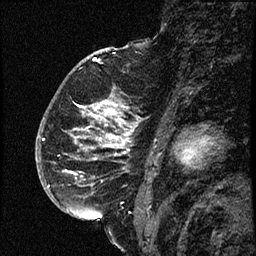
Breast MRI (dynamic contrast-enhanced), one sagittal slice; dynamic contrast-enhanced study with each time point stored as its own series, time point 2 of 3 at this slice position (early post-contrast, ordered by acquisition time); 1.5 T; TE 4.2 ms, TR 17.6 ms; 256 × 256 image matrix, field of view 200 × 200 mm. Female patient. Case-level facts recorded for this patient, not image findings: setting: breast cancer imaged before/during neoadjuvant chemotherapy; receptor status: HER2-positive.
Structures marked on this image (semi-automatically segmented with operator editing):
- analysis volume of interest (the breast-tissue region the enhancement analysis was run in; not a lesion): bounding box <52,69,144,209> (left, top, right, bottom; pixels)
- tumour enhancement mask (voxels above the 100 % enhancement threshold inside the analysis volume of interest): <71,96,137,175>